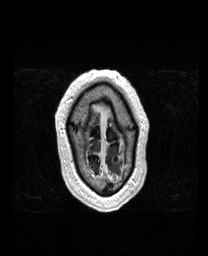
Brain MRI from a brain-tumour surgery series, one axial slice; slice 159 of 192 in the series (ordered by position); T1-weighted post-contrast; 208 × 256 image matrix, field of view 211 × 260 mm. Case-level facts recorded for this patient, not image findings: histopathology: Metastatic Carcinoma from Lung Adenocarcinoma; tumour location: Left Frontal.
Annotated regions visible in this slice (manually delineated by an expert):
- tumour: bounding box [x1, y1, x2, y2] px = [116, 158, 118, 160]